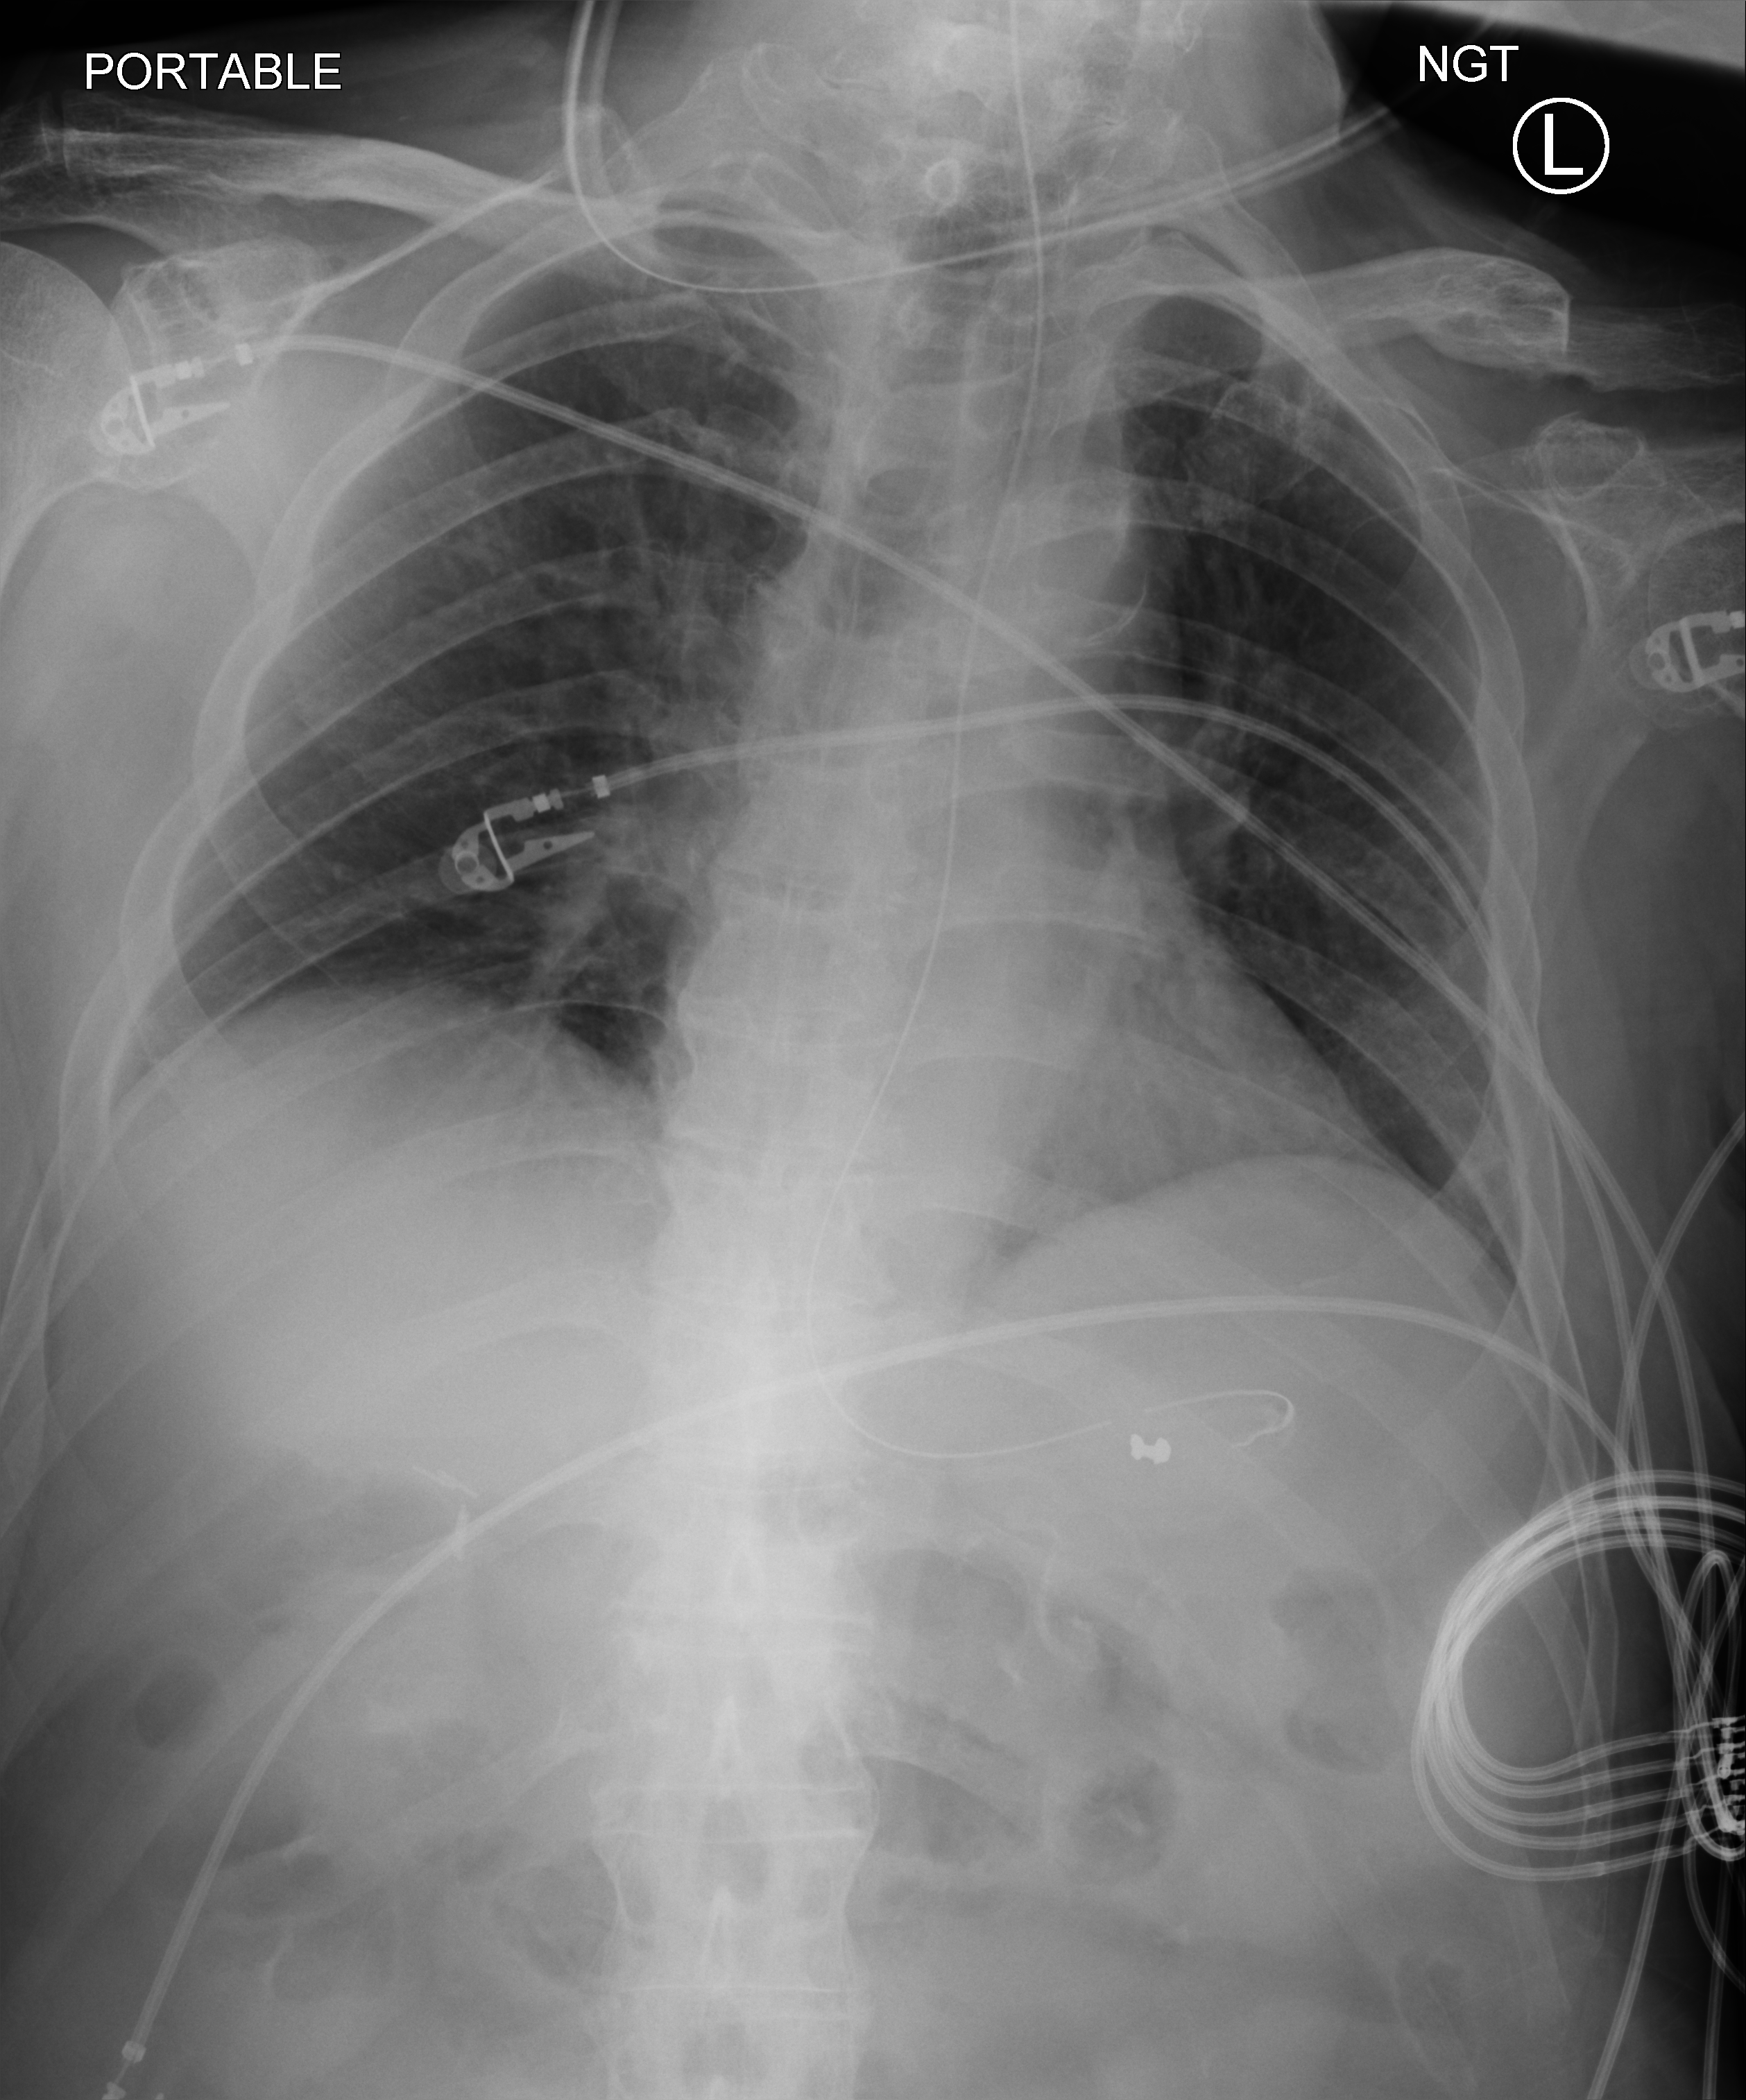
Bedside chest radiograph (computed radiography); anteroposterior (AP) projection. Patient hospitalised with COVID-19; male, aged 60–74 years.
Admission-level facts for this patient (not findings on this image; timing relative to this image not recorded): admitted to intensive care during this hospital stay: no; mechanically ventilated during this hospital stay: no.